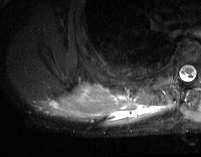
MRI of an extremity soft-tissue mass, one axial slice; position 18 of 74 along the scan axis; STIR; MR volume resampled by the dataset authors to the PET/CT grid (not the native acquisition matrix); 201 × 157 image matrix. Male patient. Case-level facts recorded for this patient, not image findings: histological type: pleiomorphic spindle cell undifferentiated; grade: high; site of the primary tumour: right parascapusular.
Outlined on this slice (expert contour drawn on MRI and transferred to this co-registered scan by the dataset authors):
- gross tumour volume including surrounding oedema: bounding box <40,82,168,126> (left, top, right, bottom; pixels)
- gross tumour volume (mass): <67,84,107,117>